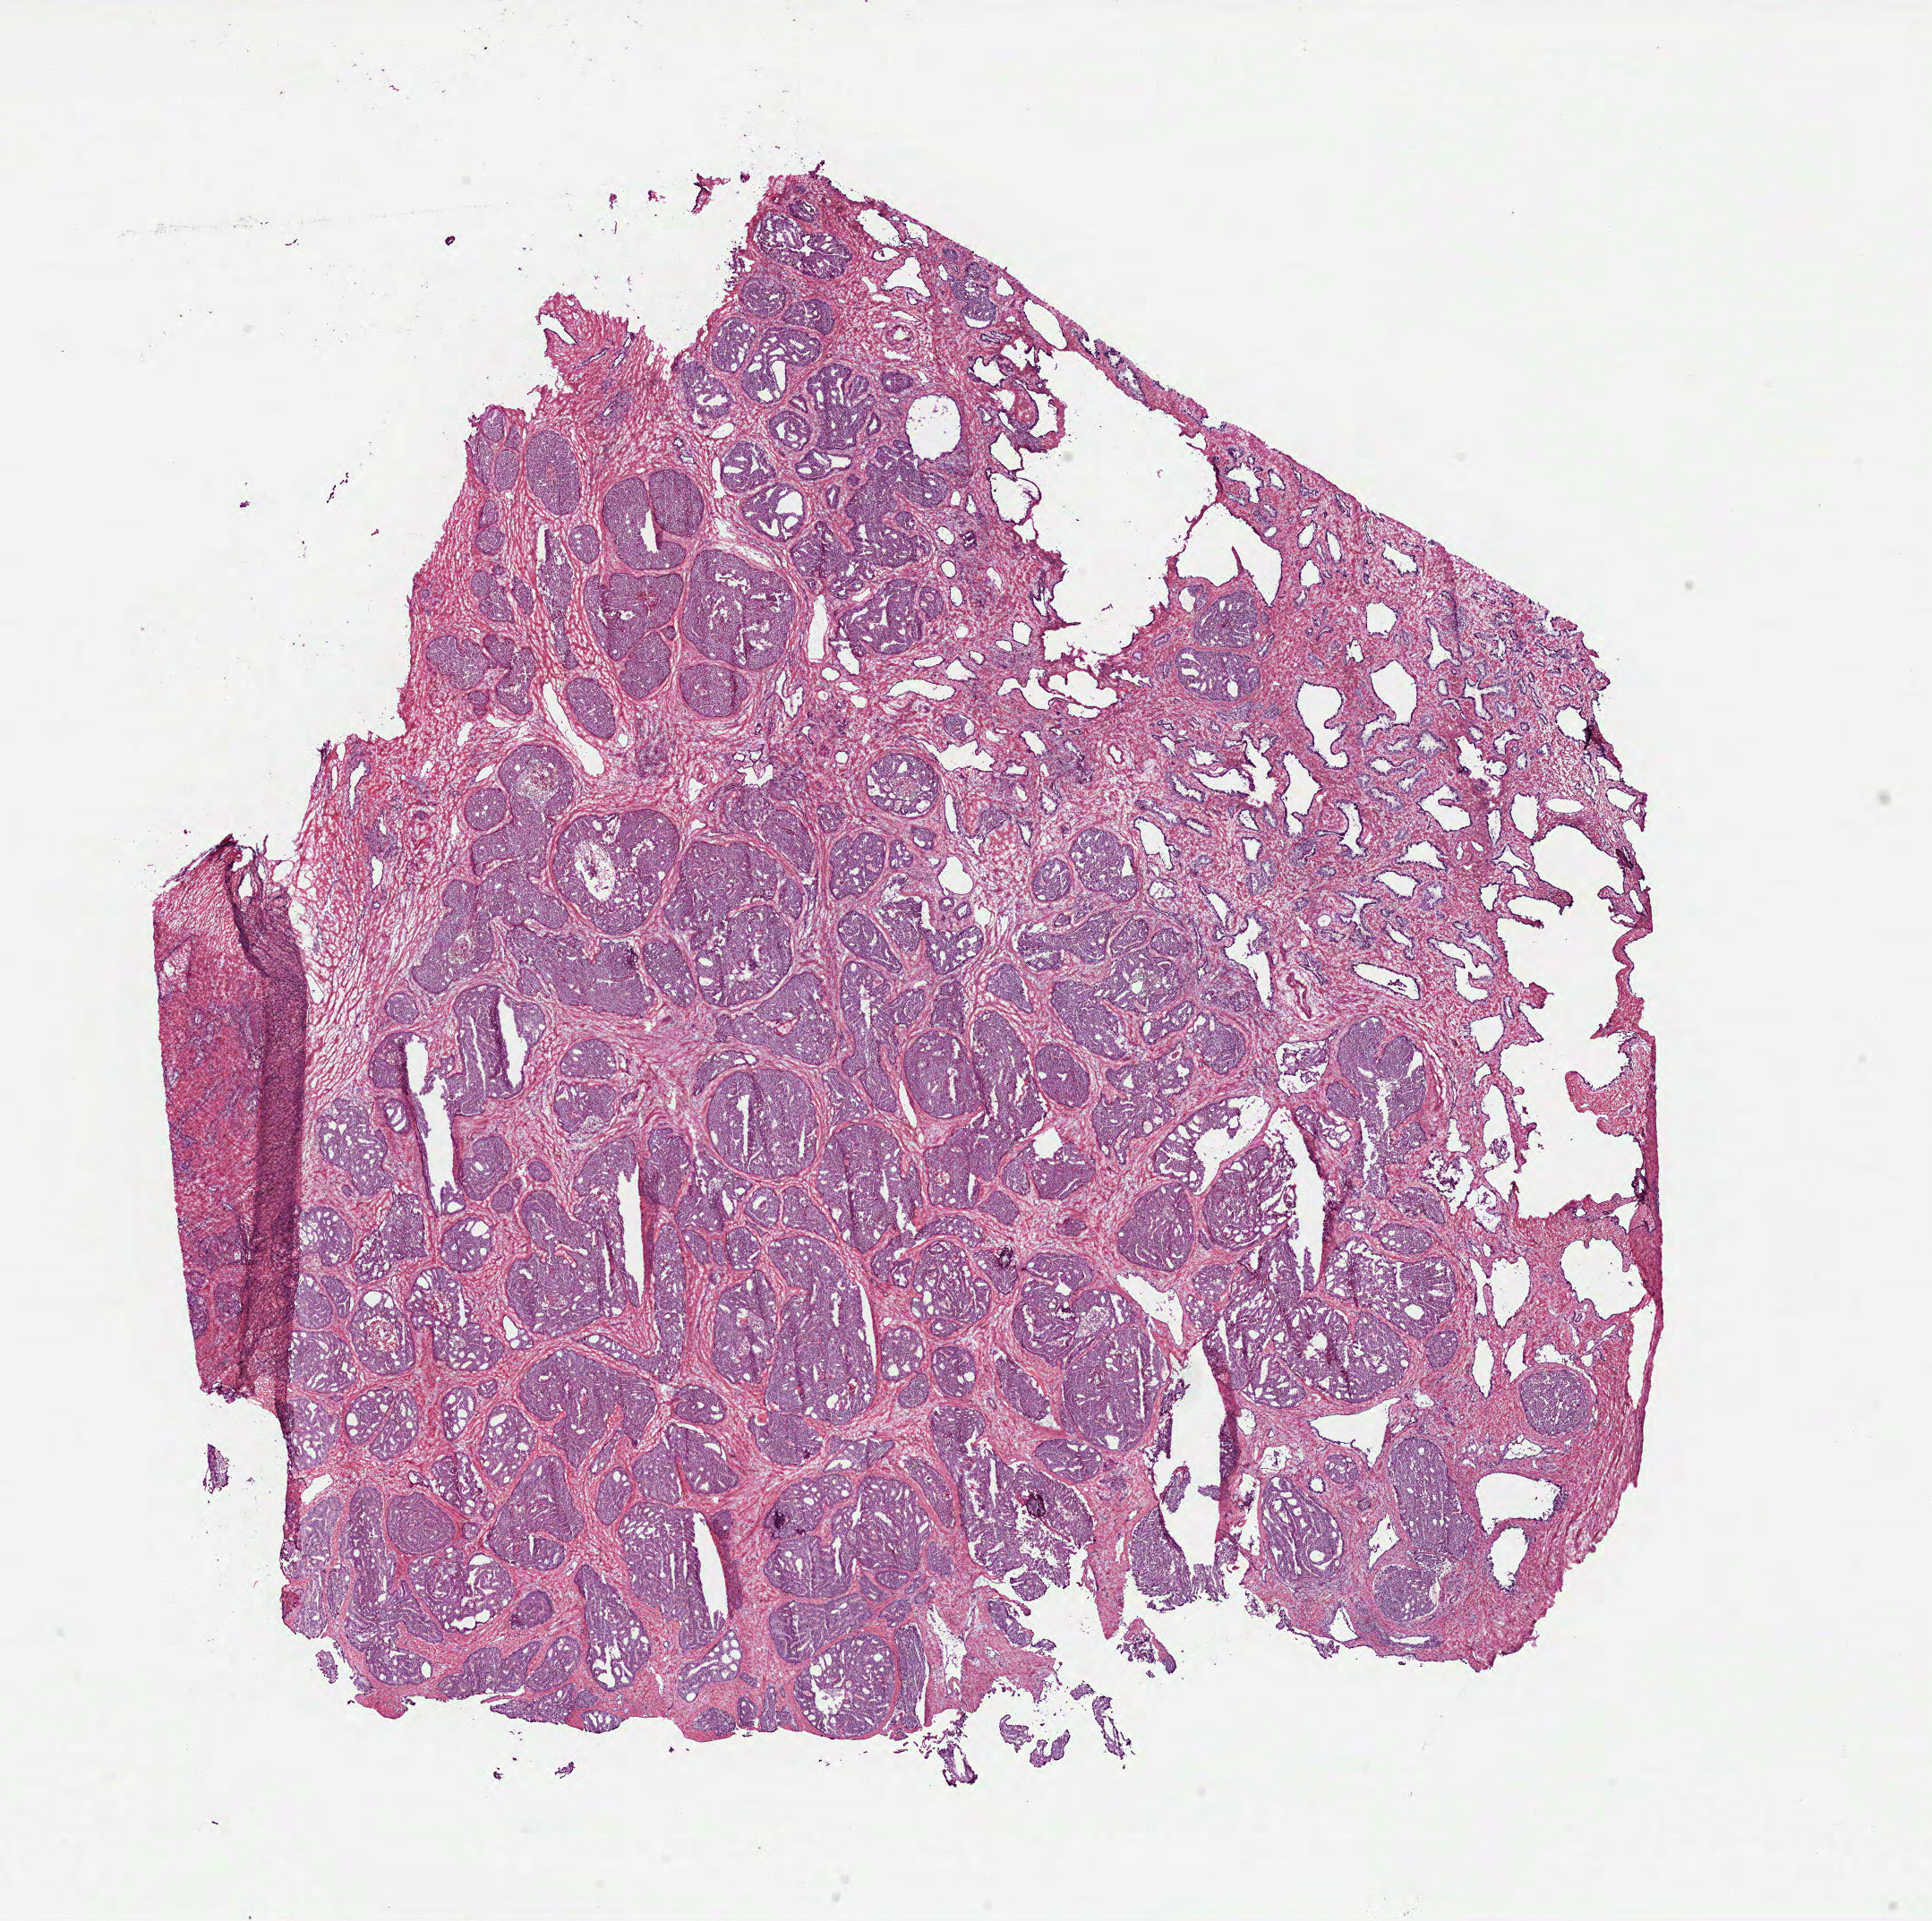
Digitized H&E tissue section (whole slide) — low-resolution overview of the scanned area, about 17.4 x 17.3 mm. Frozen section from the top of the tissue portion. Primary tumour sample from the prostate. Male patient; age at initial diagnosis 71 years. Gleason score: 8 (4+4). Pathologist review of this section (percent, as recorded): tumour cells 70%, tumour nuclei 80%, normal cells 10%, stromal cells 19%, necrosis 1%. Infiltration values recorded for this section: lymphocyte infiltration 1%, monocyte infiltration 0%, neutrophil infiltration 0%.
Lymph nodes positive (case pathology): 0 of 17 examined. Laterality: bilateral. Histologic diagnosis: Acinar cell carcinoma (prostate gland).